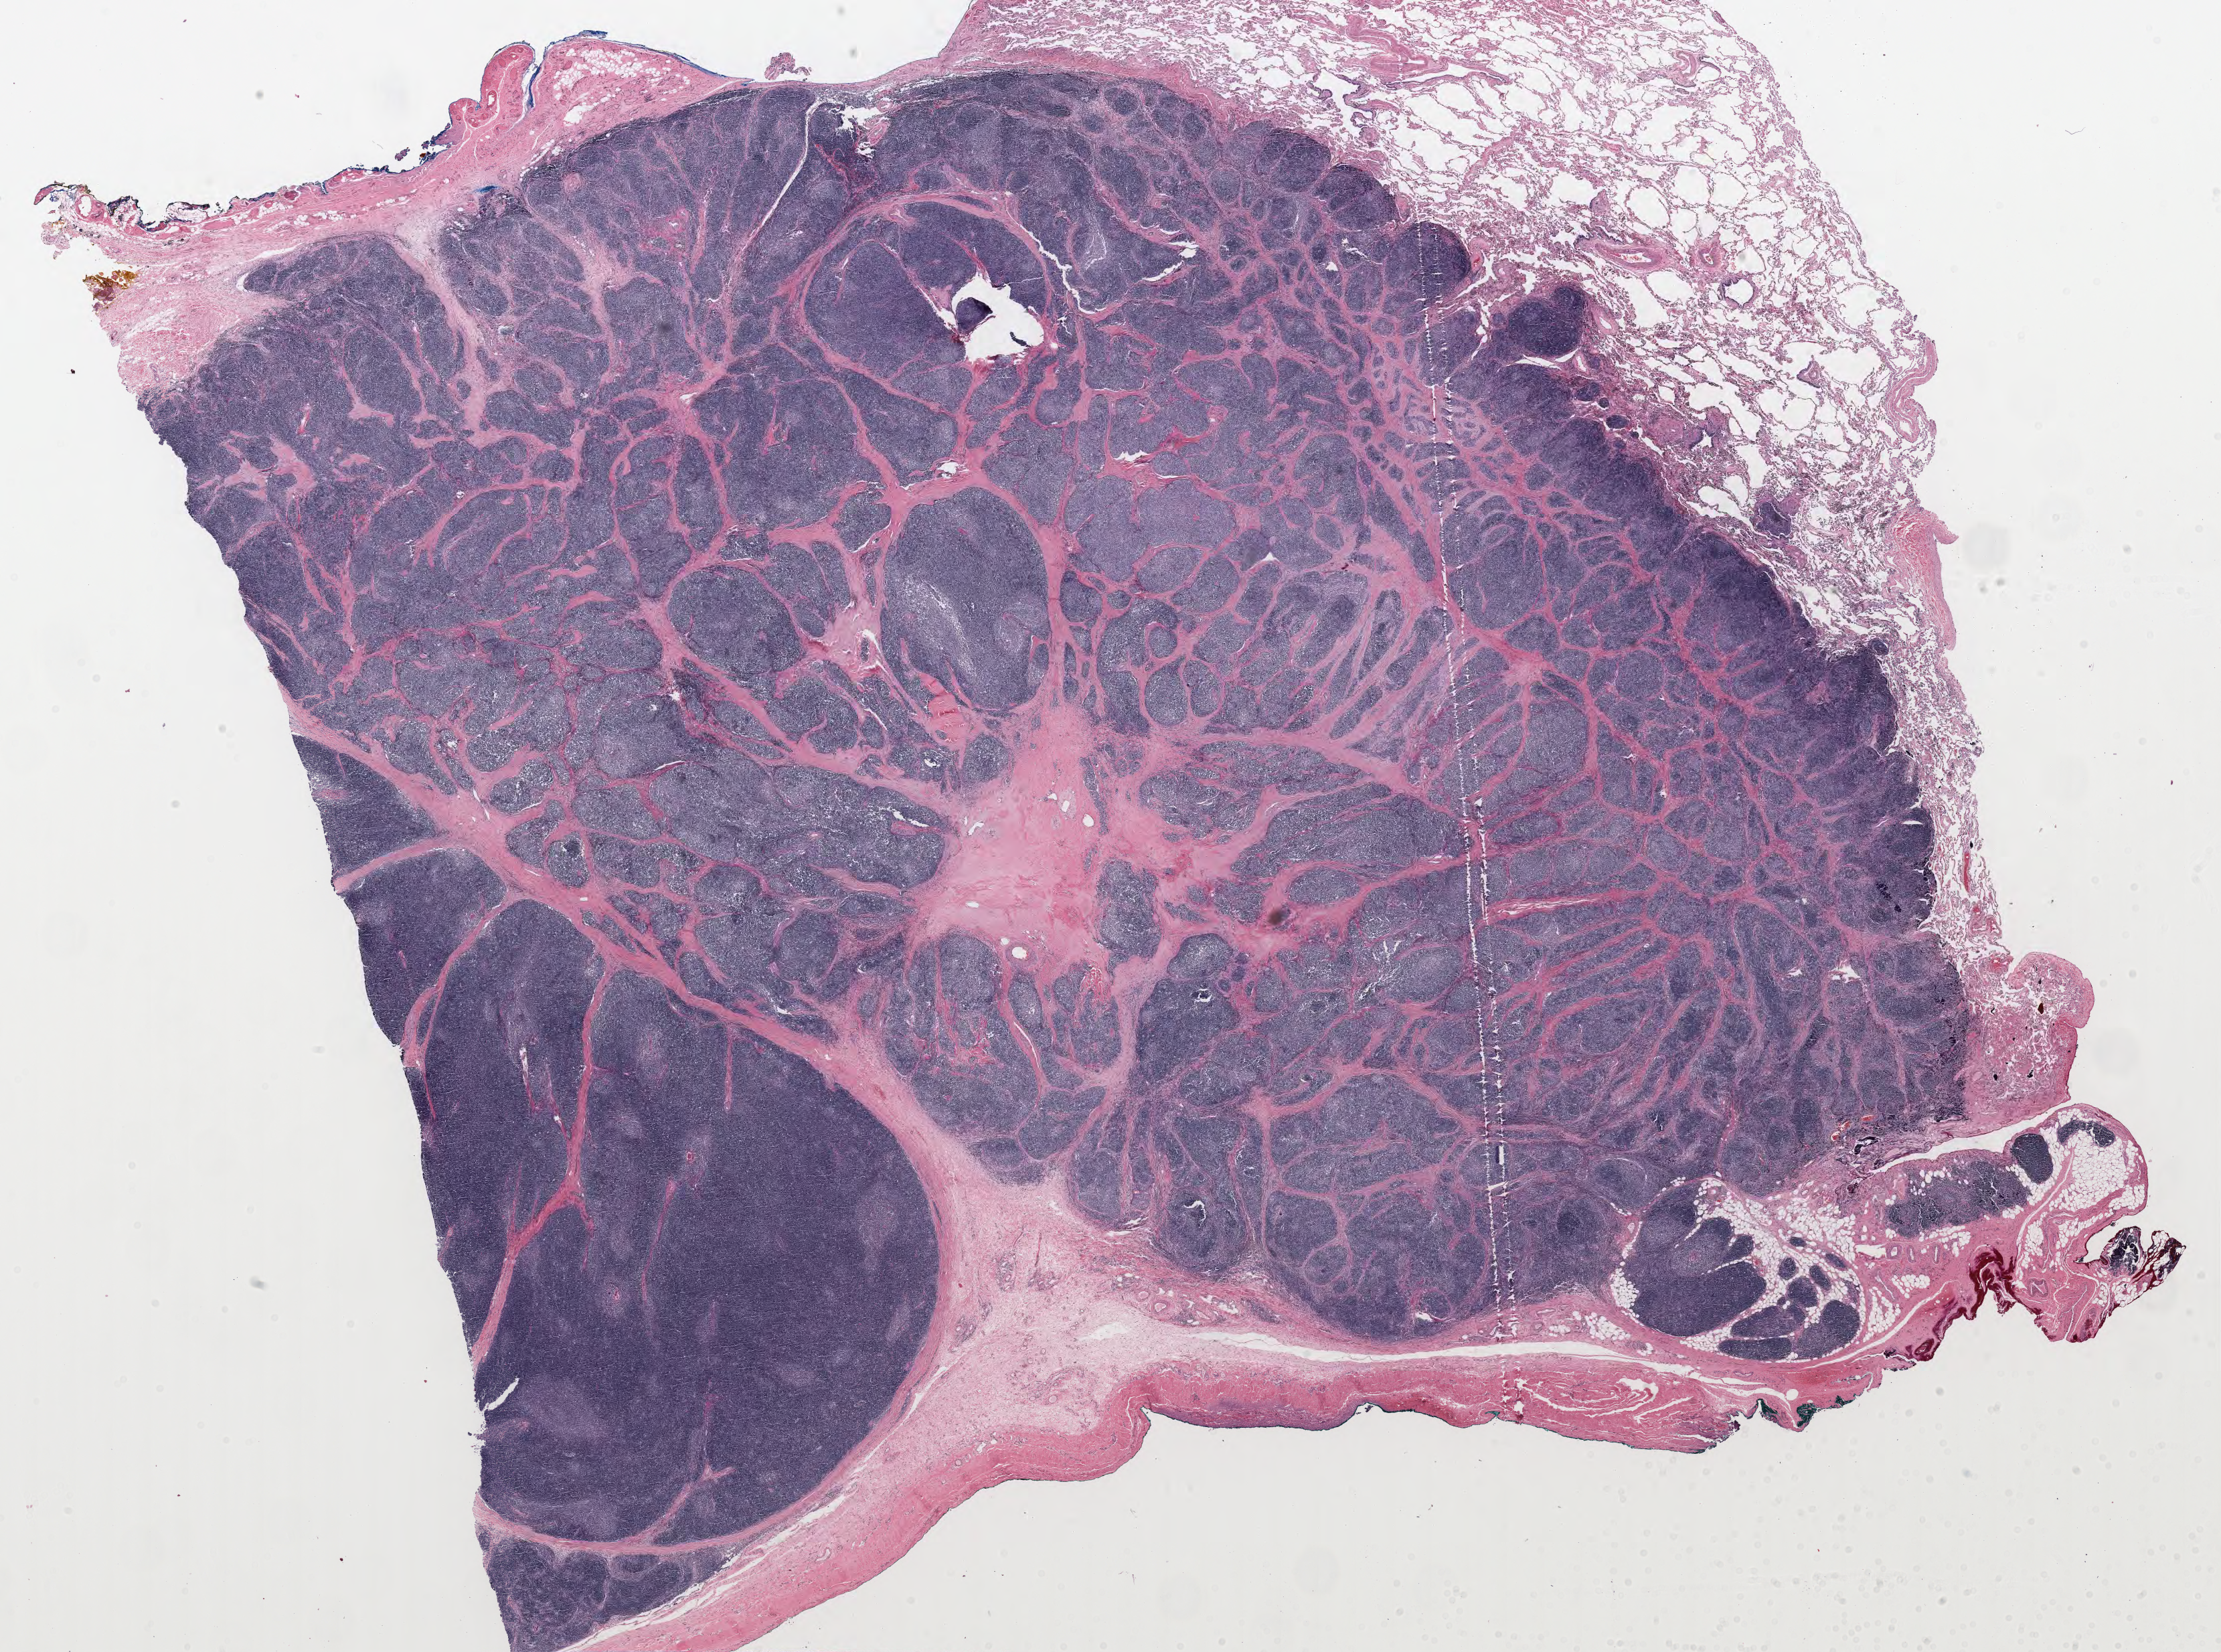
Digitized H&E-stained tissue section (whole slide), a low-resolution overview of the entire scanned area, about 26.3 x 19.6 mm. Formalin-fixed paraffin-embedded (FFPE) diagnostic section. Thymus, primary tumour sample. Patient: female, age at initial diagnosis 57 years.
• histologic diagnosis: Thymoma, type B1, NOS